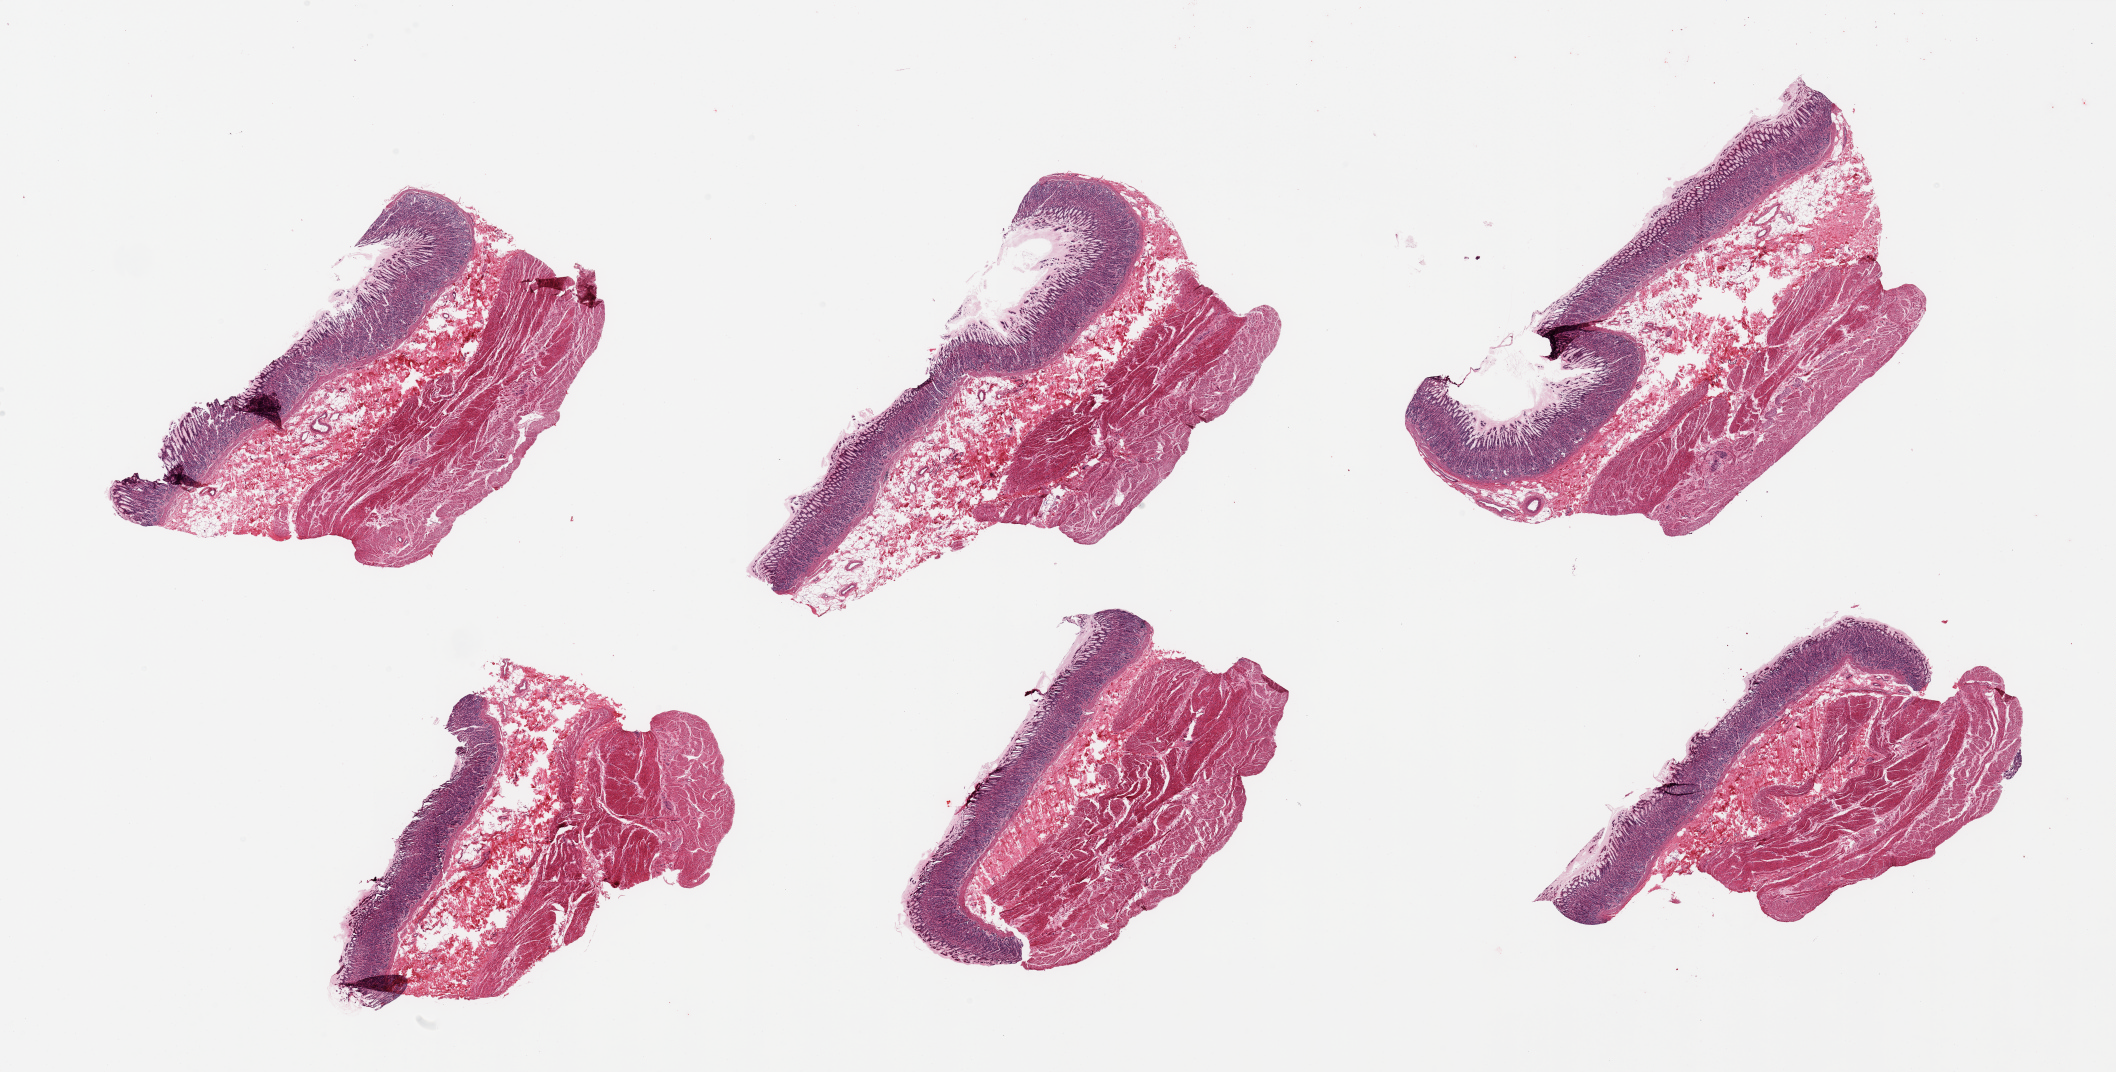
Haematoxylin and eosin whole-slide image — a low-resolution overview of the entire scanned area, about 33.5 x 17.0 mm, PAXgene-fixed, paraffin-embedded tissue, target tissue: stomach, donor tissue sample. Male donor.
- review note (as recorded): 6 pieces; full thickness sections